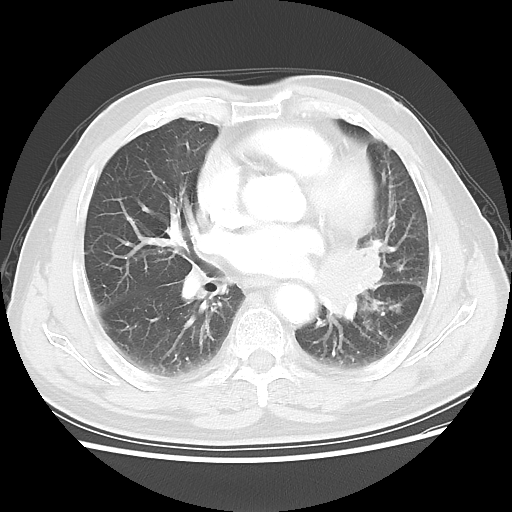
Chest CT, one axial slice. Slice 29 of 56 in the series (ordered by position). Reconstruction kernel LUNG. 120 kVp. Lung window (W 1500 / L -600 HU). 5 mm slice thickness. 512 × 512 image matrix, field of view 360 × 360 mm. Patient: male, 75 years. From the clinical record (not read from this slice): clinical TNM (as recorded): T3 N0 M0.
Outlined on this slice (bounding box drawn by a radiologist):
- lung tumour (recorded histology: squamous cell carcinoma): box from (x=310, y=239) to (x=393, y=321) px